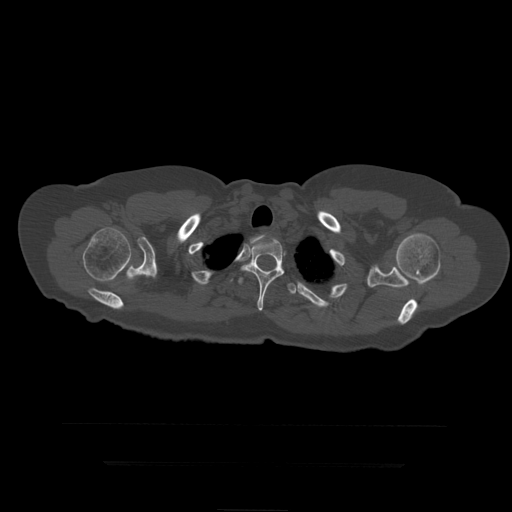
CT including the spine, one axial slice. Slice 363 of 399 in the series (ordered by position). 120 kVp. Bone window (W 1800 / L 400 HU). 512 × 512 image matrix, field of view 450 × 450 mm. Patient age 41 years. Case-level facts recorded for this patient, not image findings: primary cancer: breast.
Structures marked on this image (semi-automatic segmentation, software-assisted and operator-edited):
- T2 vertebra: bounding box (x1, y1, x2, y2) in pixels: (250, 235, 266, 245)
- T3 vertebra: (241, 237, 285, 311)
- T4 vertebra: (238, 278, 298, 294)